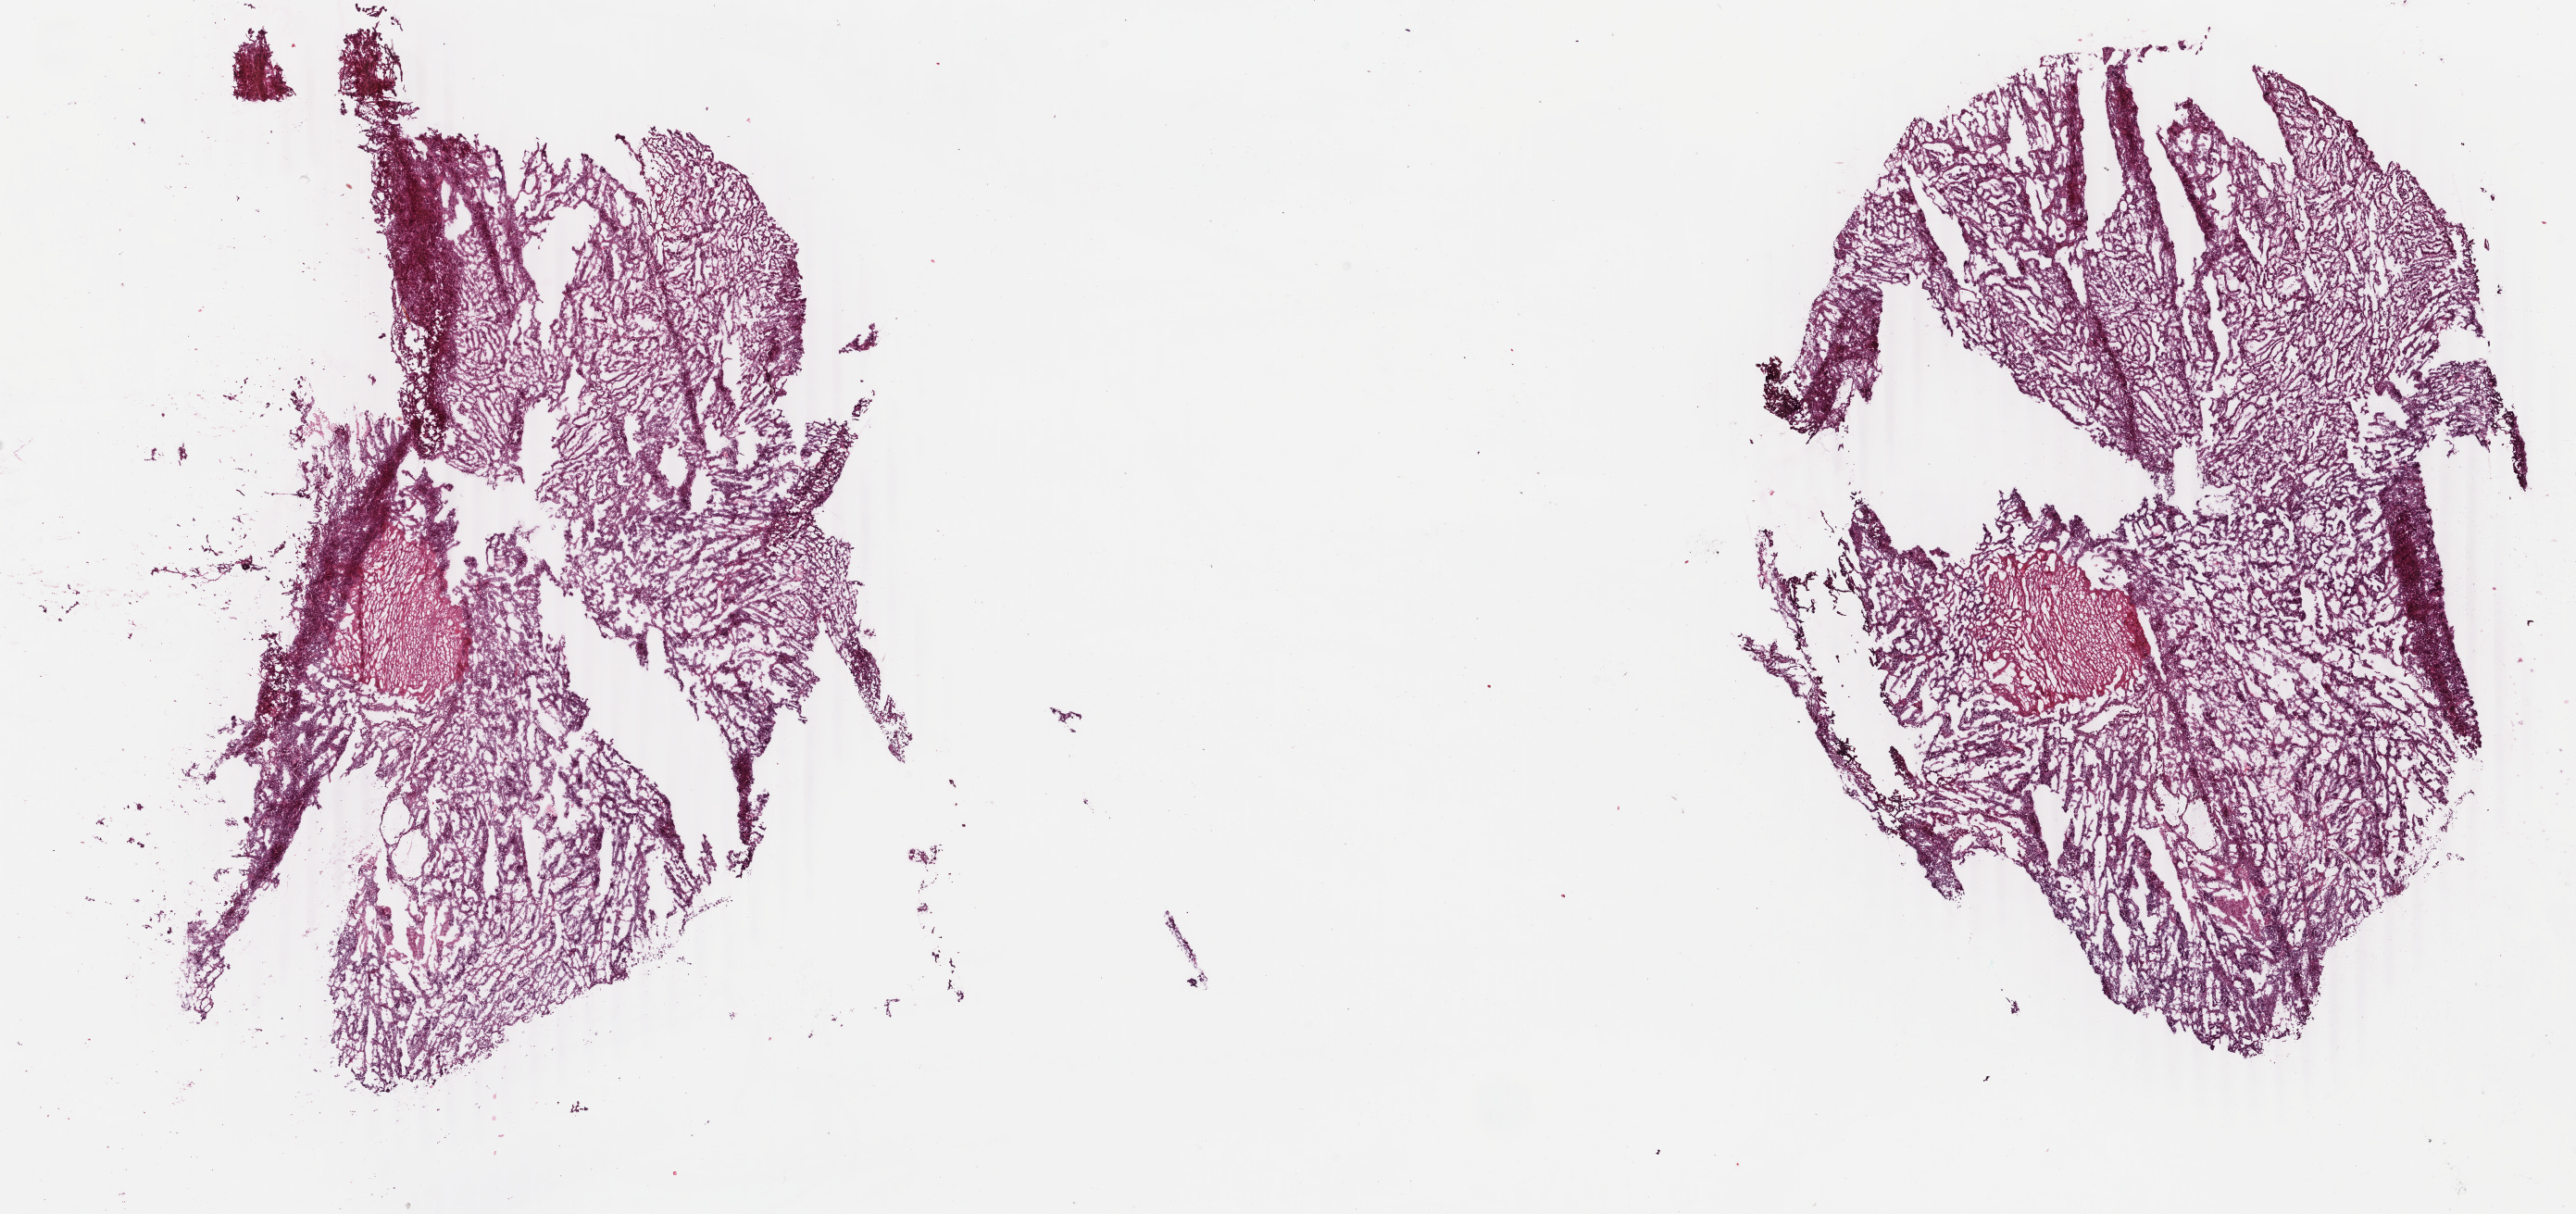
H&E whole-slide image, shown as a low-resolution overview of the whole scanned area (about 22.1 x 10.4 mm, acquisition: 40x scan), frozen section, sample: primary tumour, uterus. Patient: female, age at initial diagnosis 54 years. Histologic grade: G1 (well differentiated). Slide review estimates, as recorded: tumour cells 85%, tumour nuclei 85%, normal cells 0%, stromal cells 10%, necrosis 5%. Inflammatory infiltration, as recorded: lymphocyte infiltration 5%, monocyte infiltration 5%, neutrophil infiltration 10%.
FIGO stage: IA. Histologic diagnosis: Endometrioid adenocarcinoma, NOS (endometrium). Lymph nodes positive (case pathology): 0 of 4 examined.